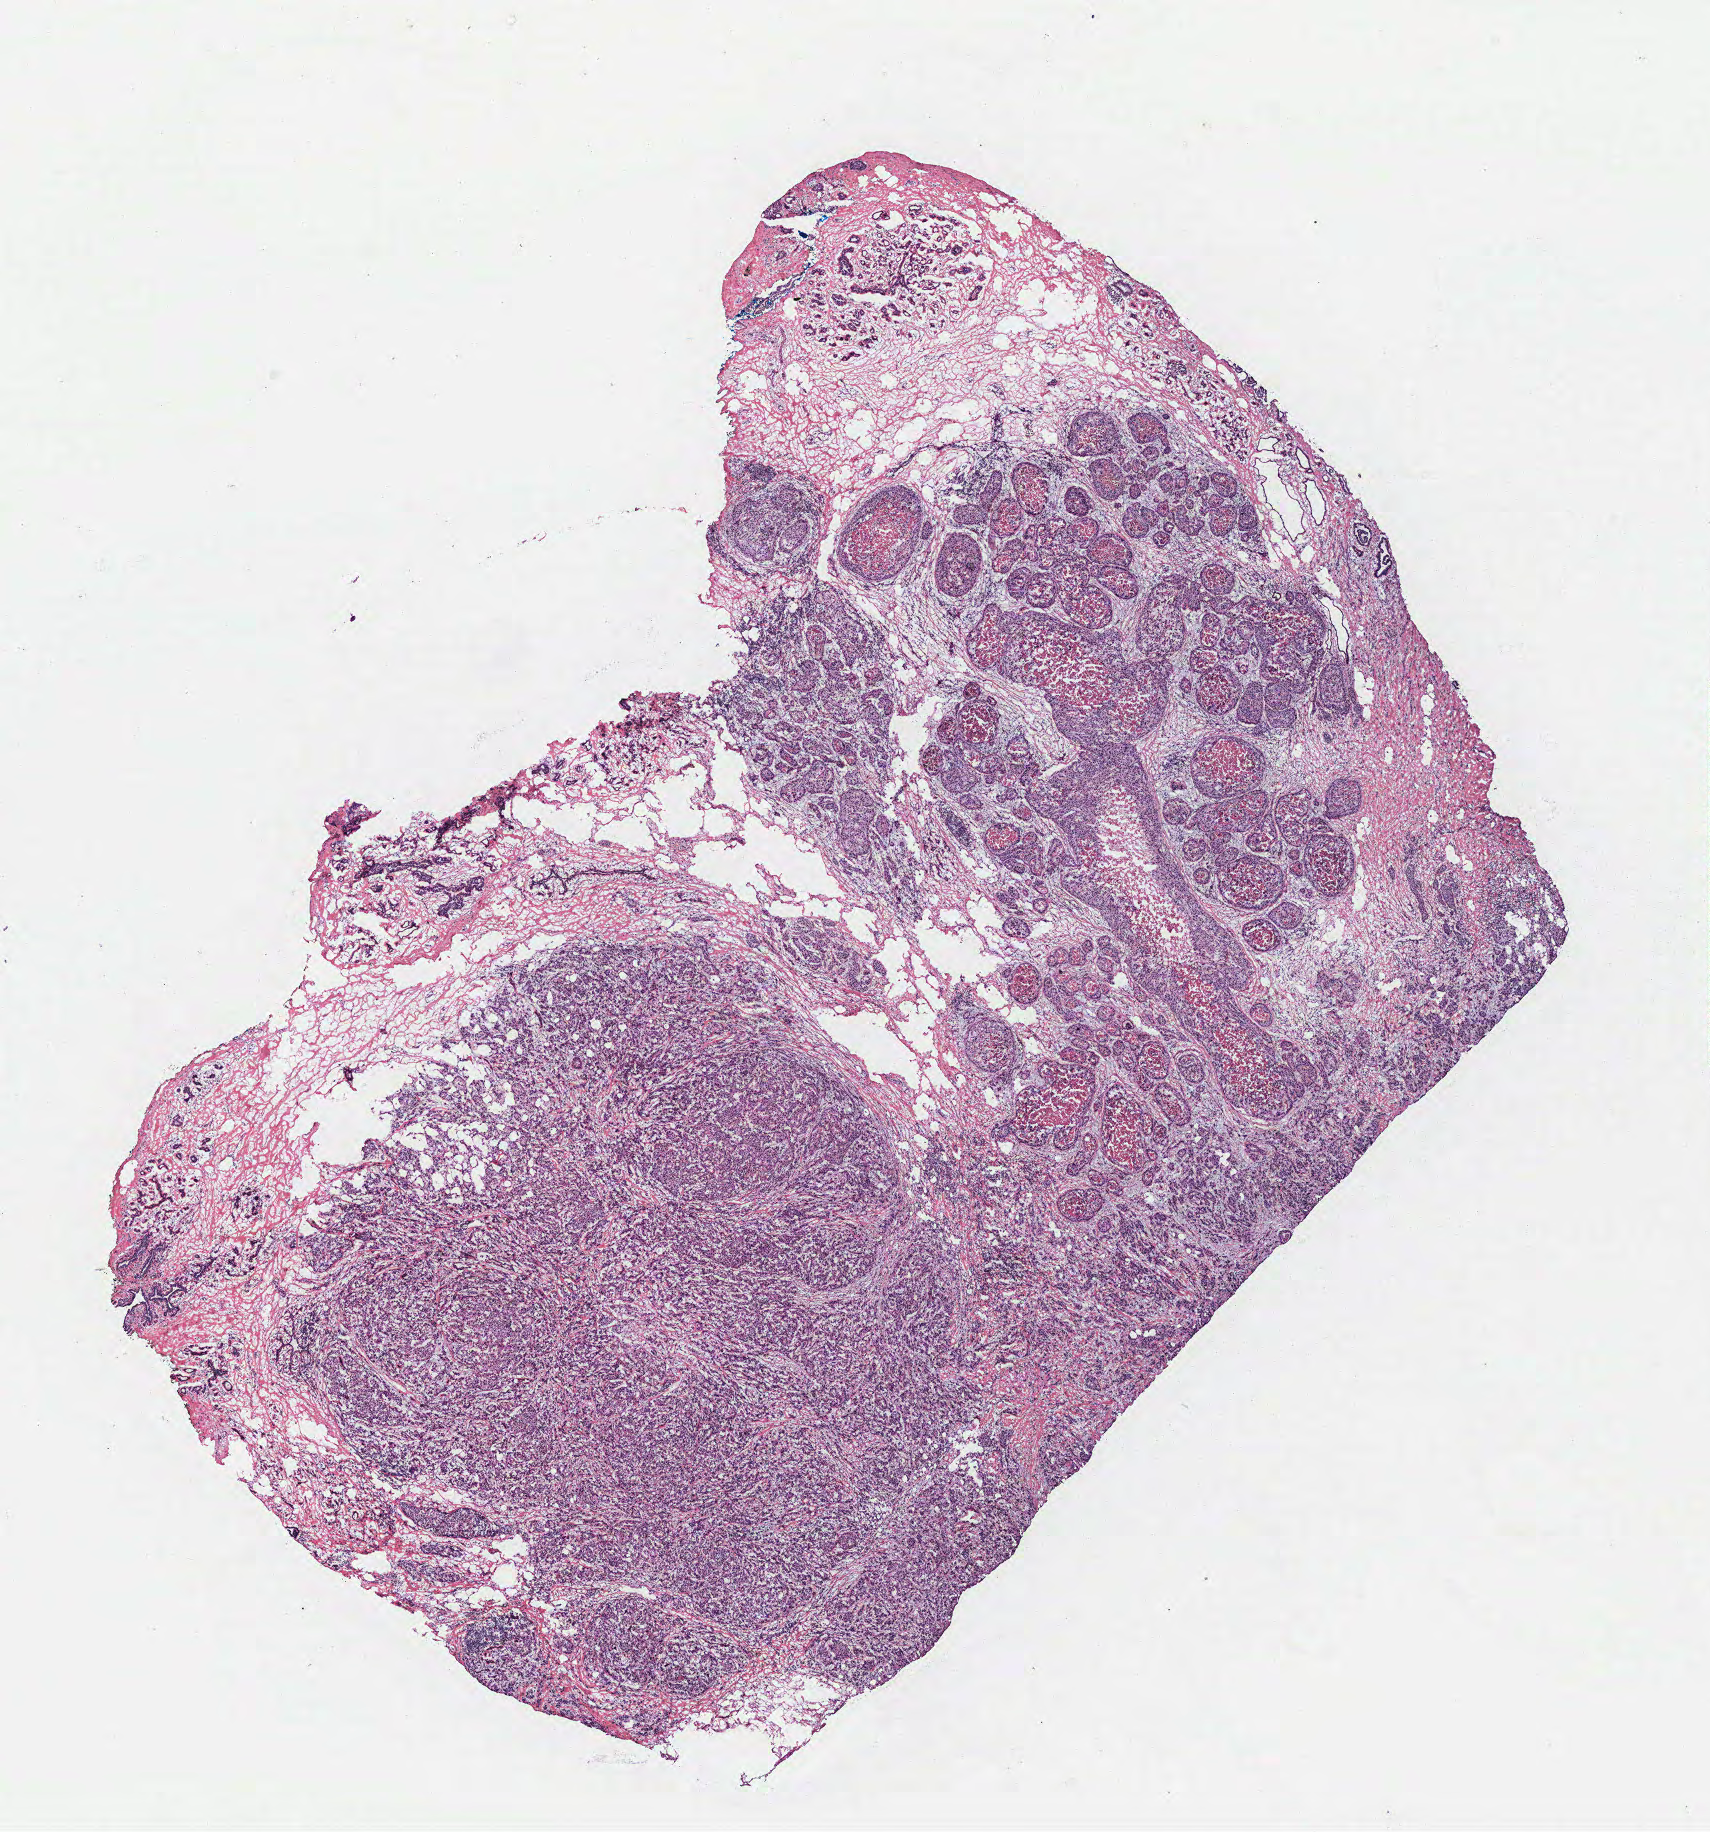
Digitized H&E tissue section (whole slide), low-resolution overview of the scanned area, about 13.7 x 14.7 mm (acquisition: 40x scan); breast, tumour tissue. Patient: female, age 46 years.
Diagnosis: Infiltrating duct and lobular carcinoma.